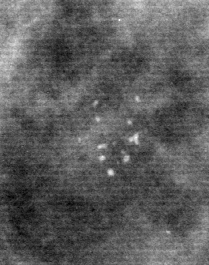
Cropped region of a digitized screen-film mammogram centred on a radiologist-marked abnormality; left breast; CC view.
Finding: calcifications, morphology punctate / pleomorphic, distribution clustered; BI-RADS assessment category 4; pathology result (as recorded, not read from the image): malignant.